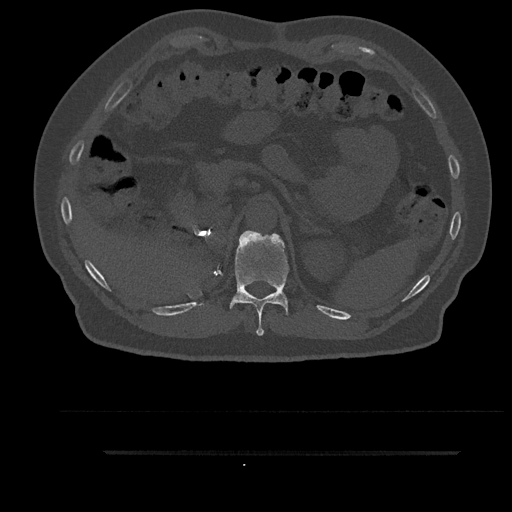
CT including the spine, one axial slice; position 298 of 797 along the scan axis; reconstruction kernel Br40s/3; 120 kVp; bone window (W 1800 / L 400 HU); 512 × 512 image matrix, field of view 432 × 432 mm. Male patient, age 63 years. From the clinical record (not read from this slice): primary cancer: renal.
Outlined on this slice (semi-automatically segmented with operator editing):
- T11 vertebra: bounding box <223,231,292,336> (left, top, right, bottom; pixels)